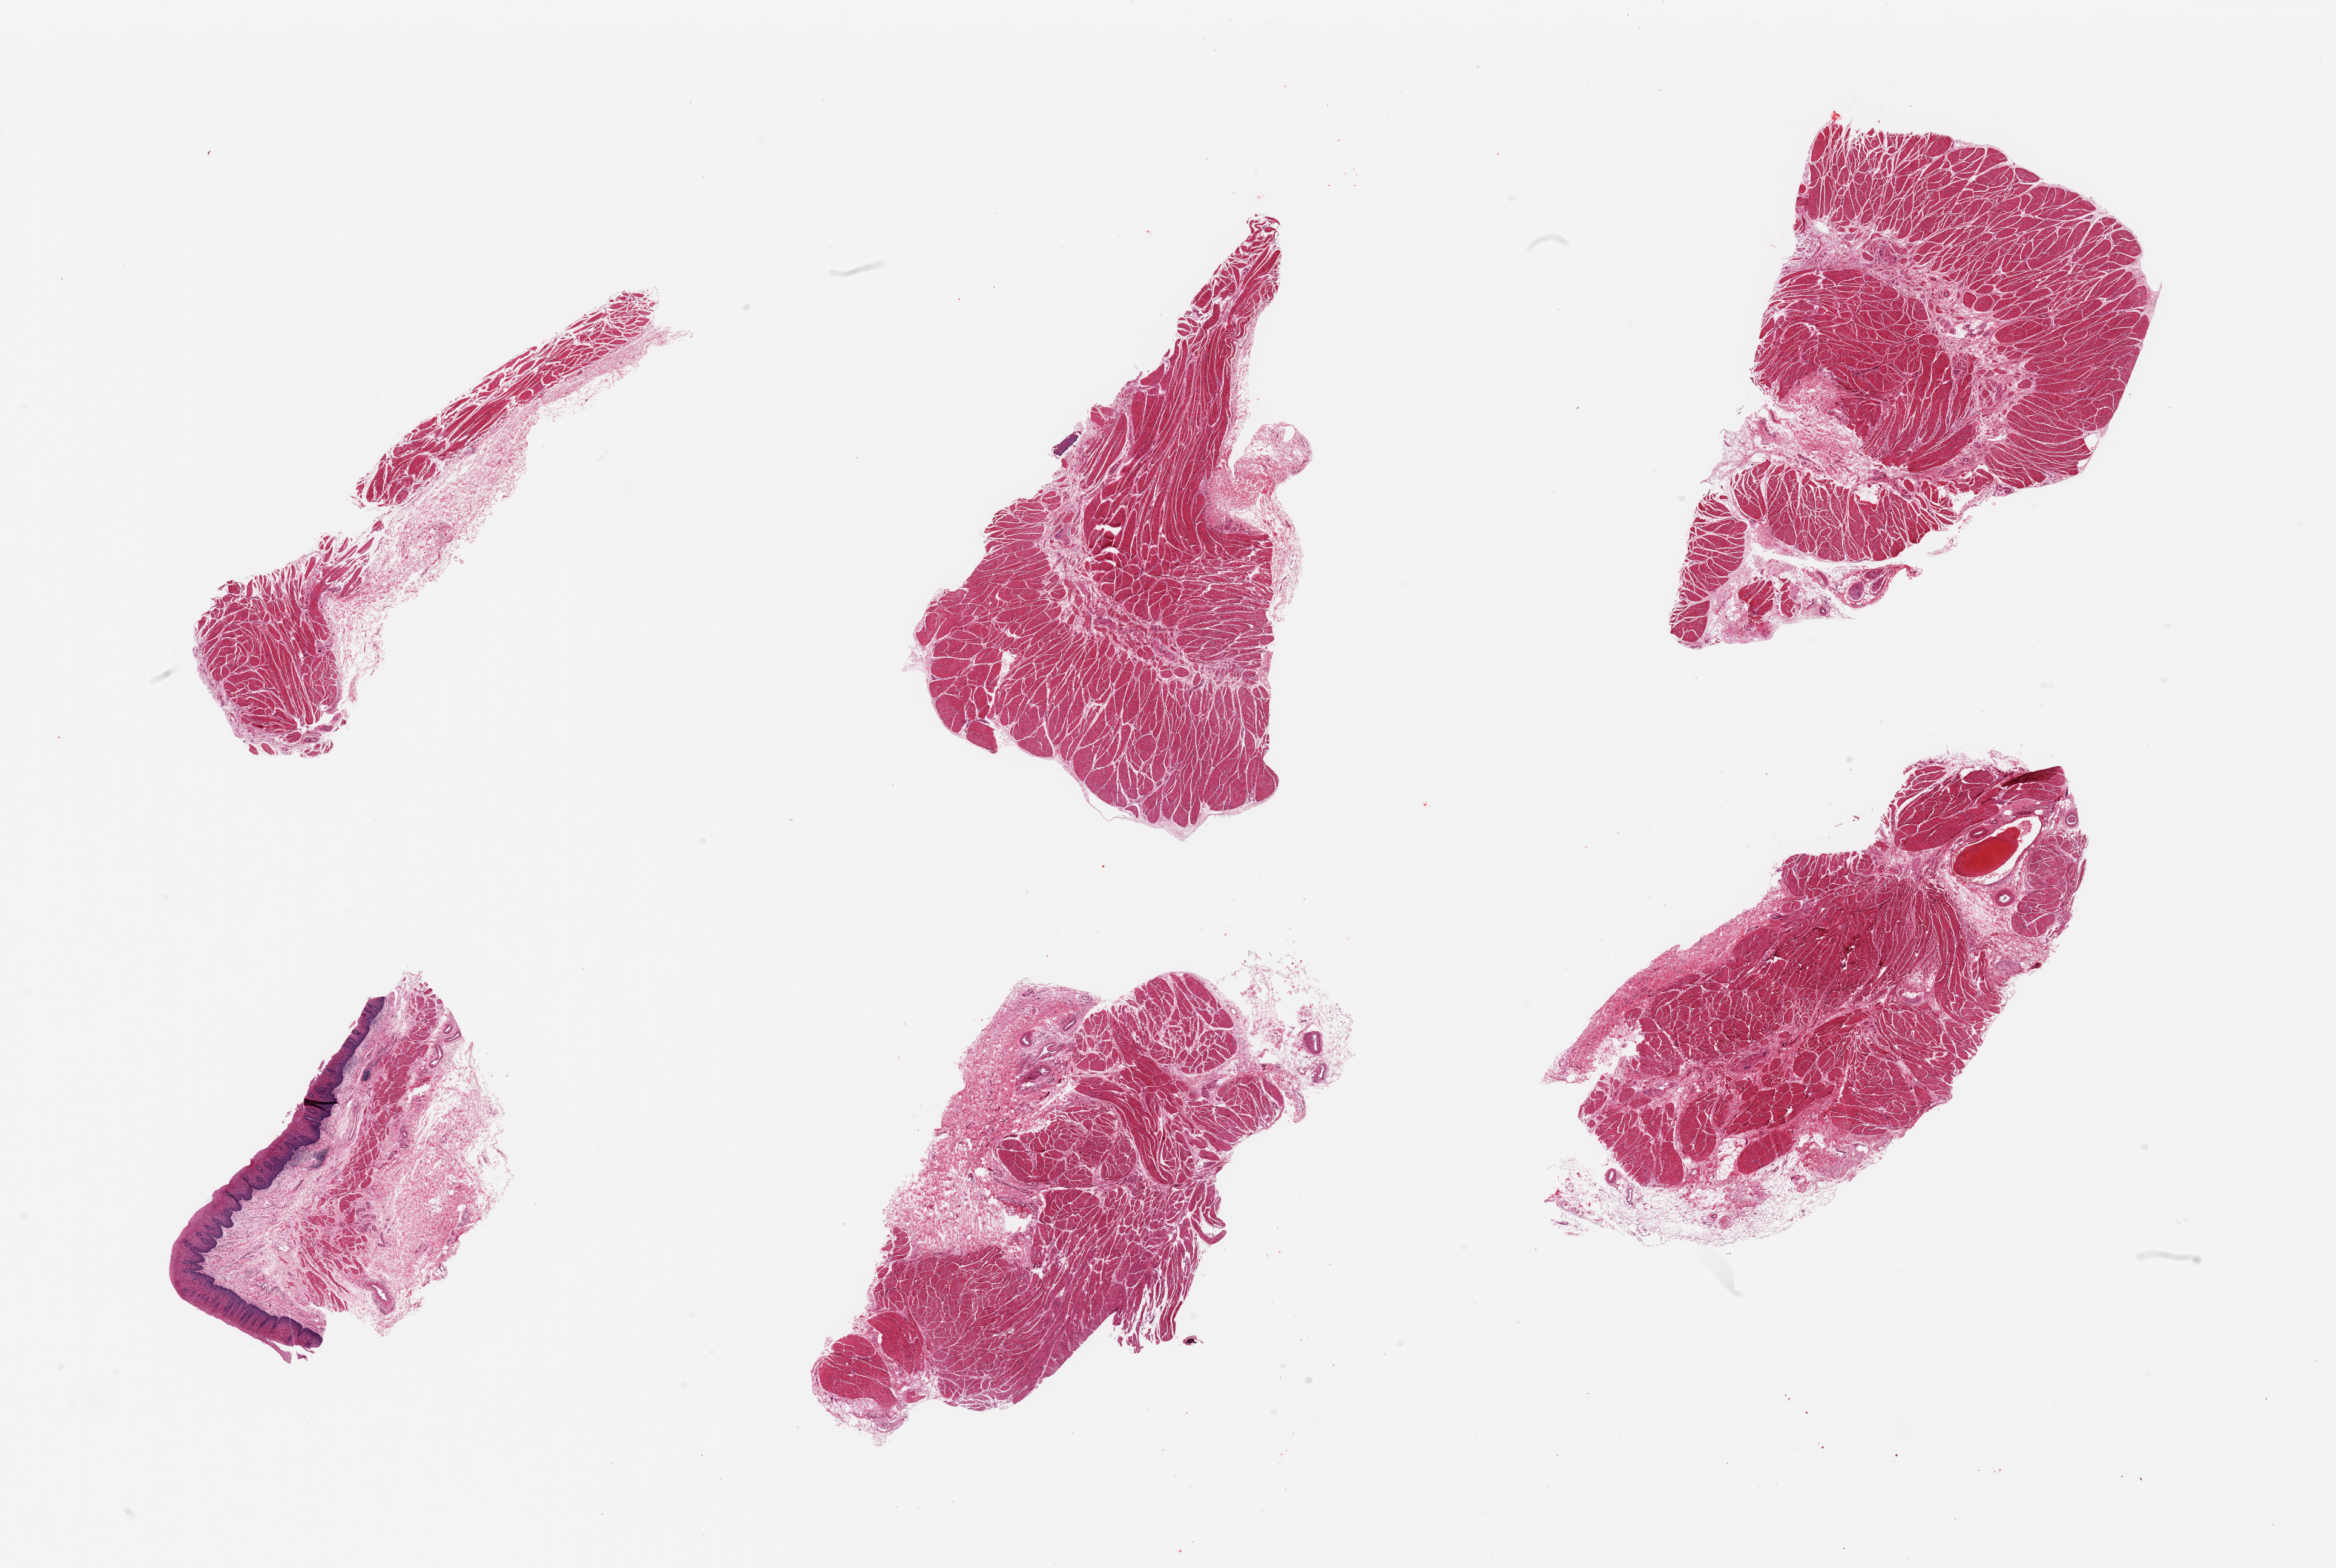
Hematoxylin and eosin (H&E) whole-slide image, brightfield — whole scanned area (about 30.5 x 20.5 mm) shown as a low-resolution overview. PAXgene-fixed paraffin-embedded (PFPE) section. Sampled site (target tissue): esophageal muscle. Donor tissue sample.
Reviewer comment on this tissue sample: 6 pieces, mainly muscularis--focal squamous mucosa present.